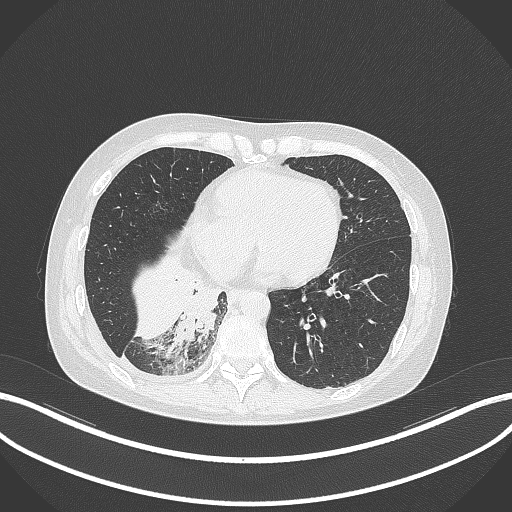
Chest CT, one axial slice. Slice 99 of 329 in the series (ordered by position). Reconstruction kernel B70f. 120 kVp. Lung window (W 1500 / L -600 HU). 1 mm slice thickness. 512 × 512 image matrix, field of view 400 × 400 mm. Female patient, age 63 years. Case-level facts recorded for this patient, not image findings: clinical TNM (as recorded): T1c N0 M0.
Annotated regions visible in this slice (bounding box drawn by a radiologist):
- lung tumour (recorded histology: adenocarcinoma): bounding box <162,272,224,355> (left, top, right, bottom; pixels)